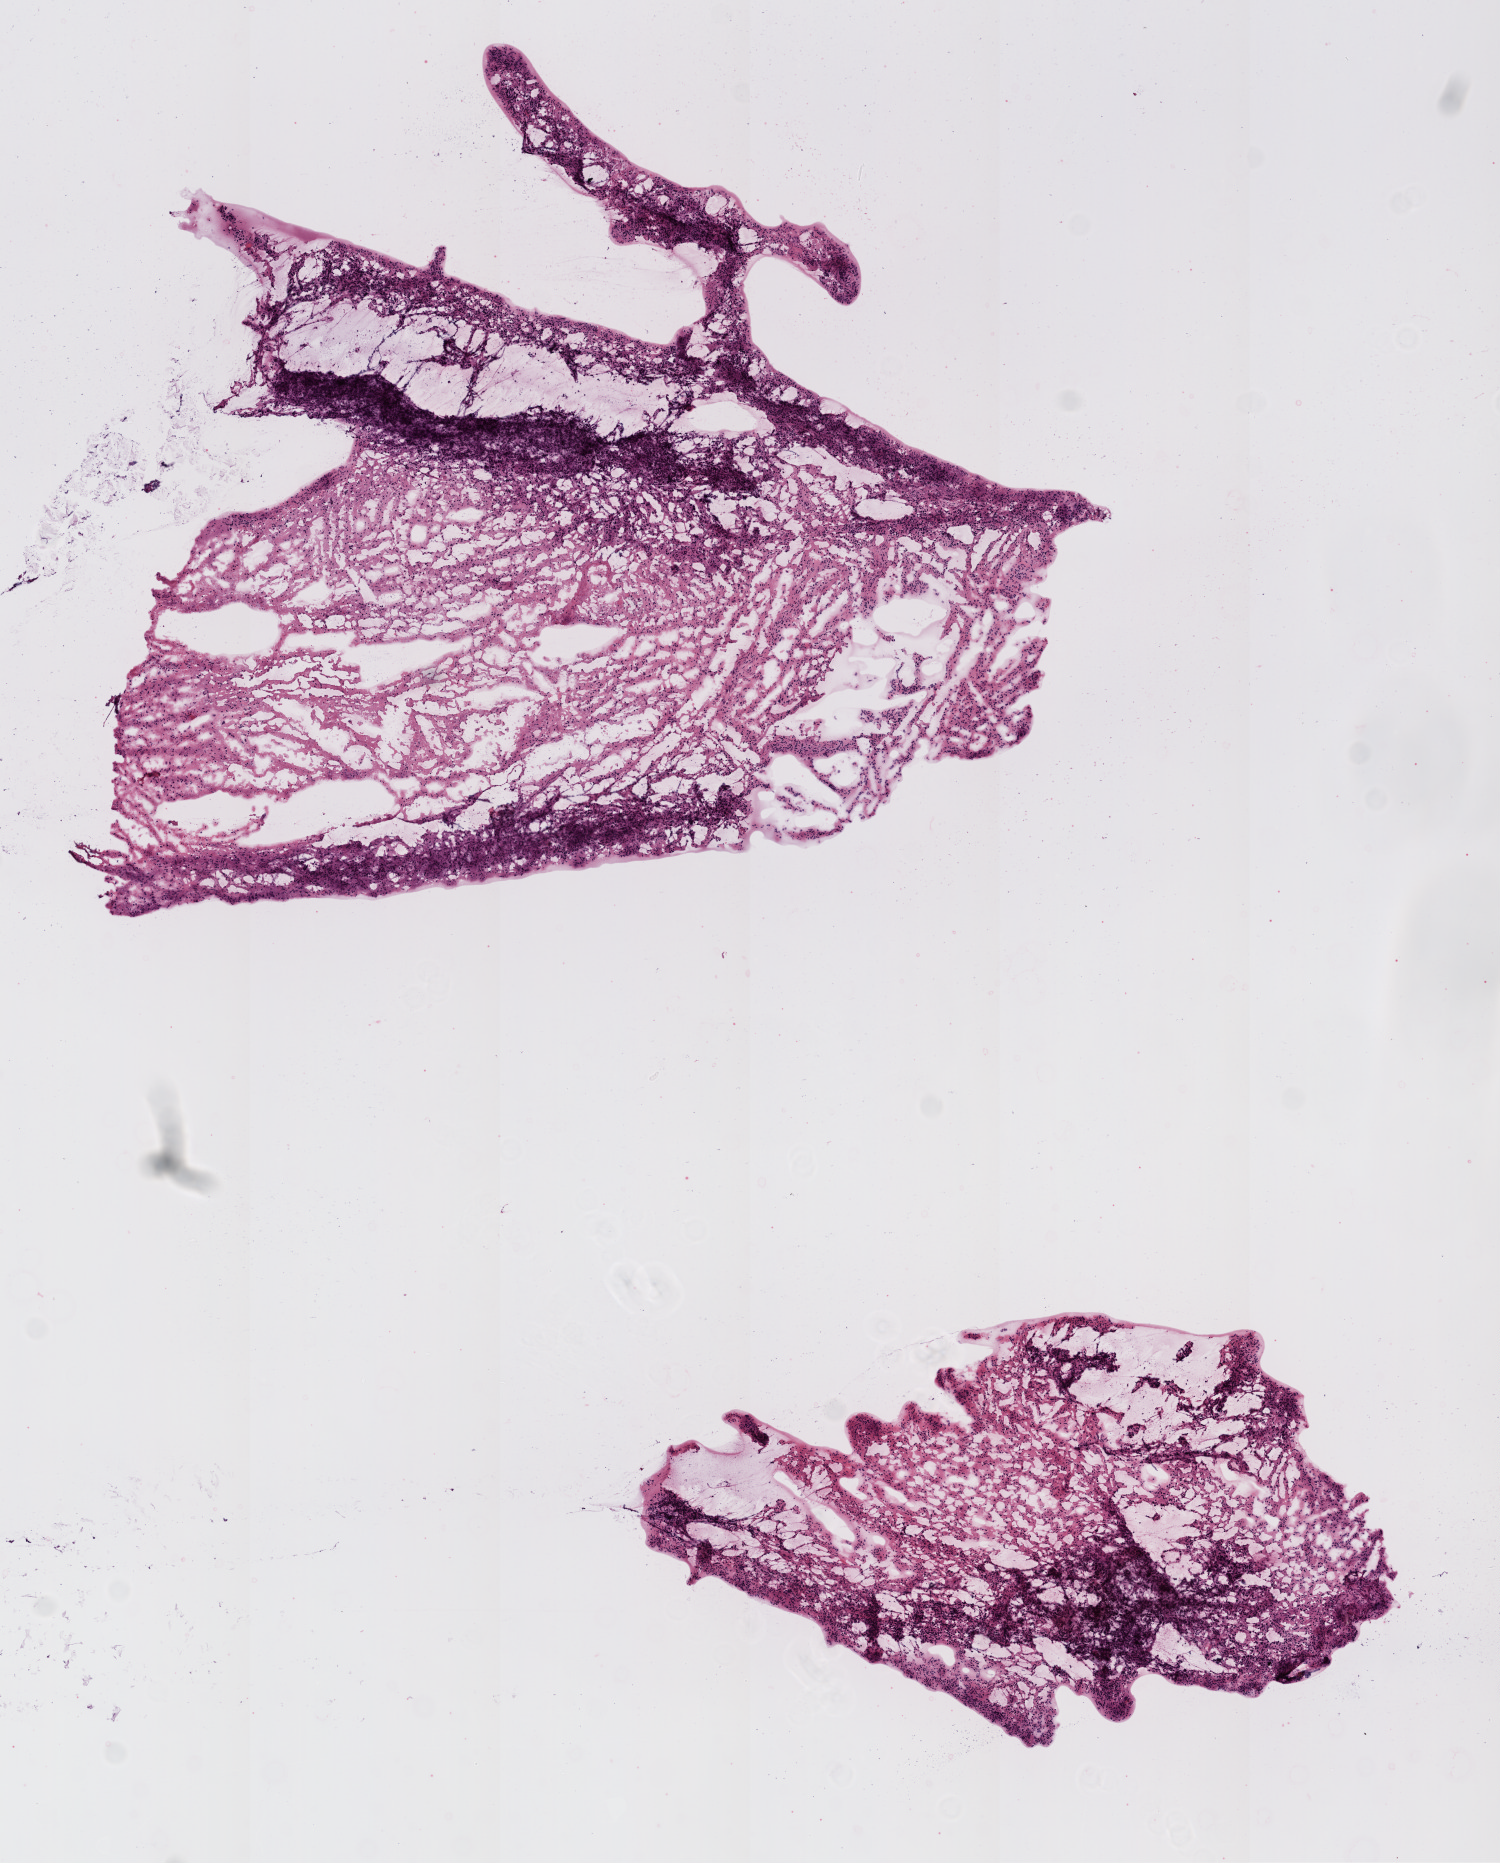
Whole-slide histology image, H&E-stained — a low-resolution overview of the entire scanned area, about 6.0 x 7.5 mm, frozen section, primary tumour sample from the brain. Male, age 74 years at initial diagnosis. Composition of this section per pathologist review: tumour cells 100%, tumour nuclei 75%, normal cells 0%, stromal cells 0%, necrosis 0%.
• histologic diagnosis: Glioblastoma